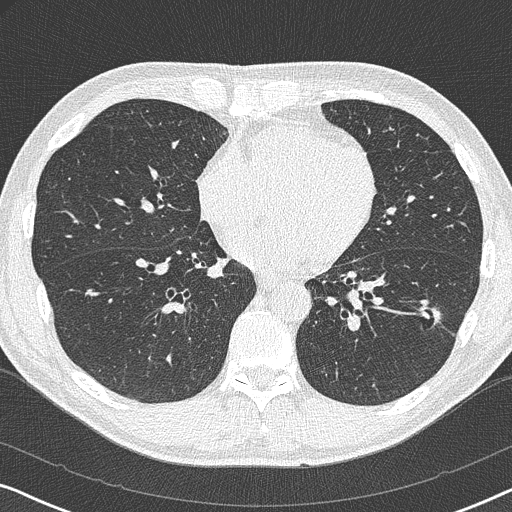
Chest CT (low-dose screening protocol), one axial image; first (baseline) screen; lung window (W 1500 / L -600 HU); 1 mm slice thickness; 120 kVp; slice 204 of 327 in the series; 512 × 512 image matrix. Male participant, aged 59 years at enrolment. Current smoker at enrolment.
Expert-annotated lung lesion, box from (x=414, y=302) to (x=451, y=341) px. The screening reader recorded 2 non-calcified nodules or masses ≥4 mm on this exam; which of them this box marks is not recorded. Later outcome: lung cancer diagnosed 821 days after this screen — adenocarcinoma, NOS, left lower lobe, poorly differentiated (G3), stage IA (AJCC 6th edition), 20 mm at pathology.